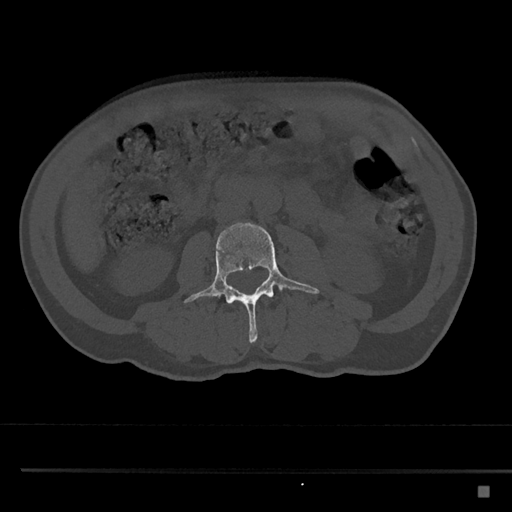
CT including the spine, one axial slice; slice 698 of 797 in the series (ordered by position); 120 kVp; bone window (W 1800 / L 400 HU); 0.5 mm slice thickness; 512 × 512 image matrix, field of view 391 × 391 mm. Male patient, age 59 years. Case-level facts recorded for this patient, not image findings: primary cancer: prostate.
Outlined on this slice (semi-automatic segmentation, software-assisted and operator-edited):
- L3 vertebra: bounding box [x1, y1, x2, y2] px = [185, 222, 319, 344]